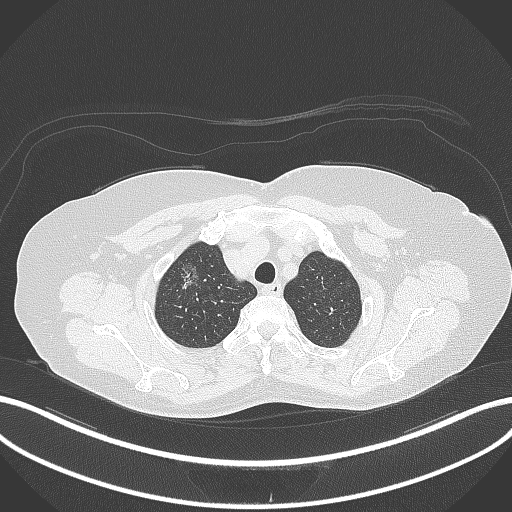
Chest CT, one axial slice; position 301 of 365 along the scan axis; 120 kVp; lung window (W 1500 / L -600 HU); 512 × 512 image matrix, field of view 400 × 400 mm. Patient: female, 62 years. From the clinical record (not read from this slice): clinical TNM (as recorded): T1c N0 M0.
Structures marked on this image (rectangle marked by the reading radiologist):
- lung tumour (recorded histology: adenocarcinoma): bounding box (x1, y1, x2, y2) in pixels: (176, 257, 210, 294)